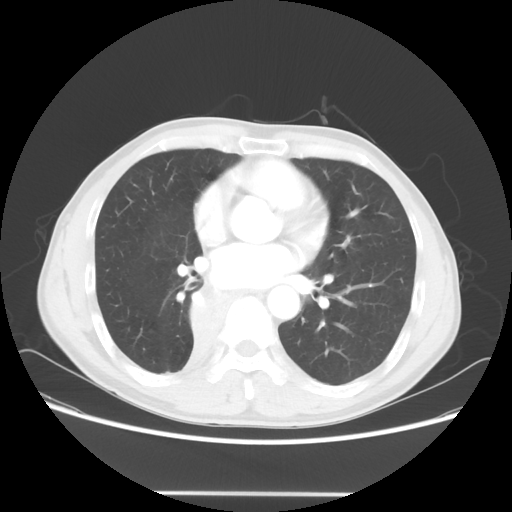
Chest CT, one axial slice; slice 29 of 62 in the series (ordered by position); reconstruction kernel STANDARD; 120 kVp; lung window (W 1500 / L -600 HU); 512 × 512 image matrix, field of view 393 × 393 mm. Patient: male, 47 years. Case-level facts recorded for this patient, not image findings: clinical TNM (as recorded): T2 N0 M0; histopathological grade: G2.
Outlined on this slice (bounding box drawn by a radiologist):
- lung tumour (recorded histology: squamous cell carcinoma): box from (x=181, y=280) to (x=226, y=379) px